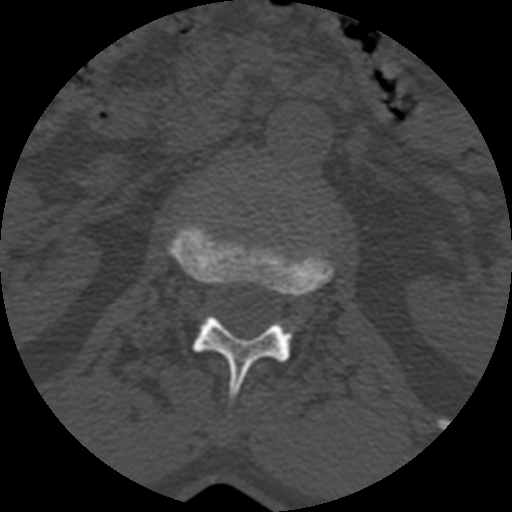
CT including the spine, one axial slice; reconstruction kernel STANDARD; 120 kVp; bone window (W 1800 / L 400 HU); 1.25 mm slice thickness; 512 × 512 image matrix. Patient age 71 years. Case-level facts recorded for this patient, not image findings: primary cancer: prostate.
Structures marked on this image (semi-automatically segmented with operator editing):
- L1 vertebra: bounding box (x1, y1, x2, y2) in pixels: (170, 222, 332, 399)